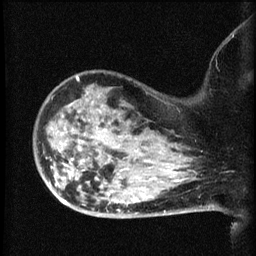
Breast MRI (dynamic contrast-enhanced), one sagittal slice; position 48 of 60 along the scan axis; dynamic contrast-enhanced series, image 2 of 3 at this slice position (ordered by acquisition); 1.5 T; TE 4.2 ms, TR 8.2 ms; 256 × 256 image matrix. Female patient, age 50 years.
Outlined on this slice (semi-automatically segmented with operator editing):
- analysis volume of interest (the breast-tissue region the enhancement analysis was run in; not a lesion): box from (x=38, y=83) to (x=169, y=211) px
- tumour enhancement mask (voxels above the 70 % enhancement threshold inside the analysis volume of interest): (x=61, y=200)–(x=66, y=204)